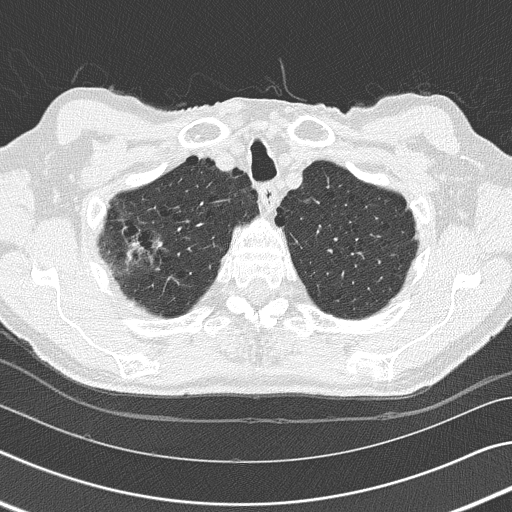
Low-dose screening chest CT, one axial slice. Position 139 of 155 along the scan axis. Reconstruction kernel B50f. 120 kVp. Lung window (W 1500 / L -600 HU). 2 mm slice thickness. 512 × 512 image matrix, field of view 340 × 340 mm.
Annotated regions visible in this slice (expert manual segmentation):
- lesion 1 (tumor, middle lobe of right lung): box from (x=126, y=237) to (x=163, y=265) px